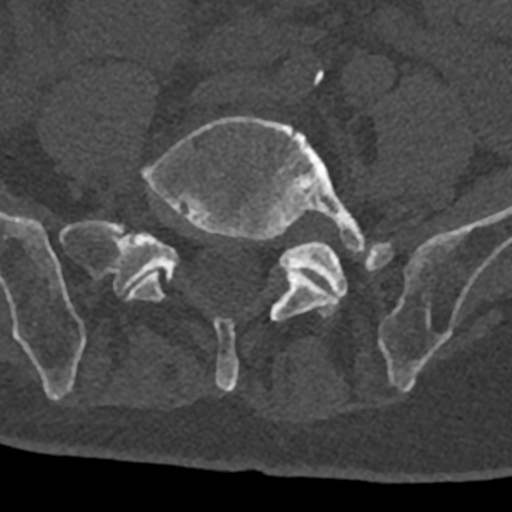
CT including the spine, one axial slice. Slice 183 of 797 in the series (ordered by position). Bone window (W 1800 / L 400 HU). 512 × 512 image matrix. Male patient, age 74 years. Case-level facts recorded for this patient, not image findings: primary cancer: renal.
Outlined on this slice (semi-automatic segmentation, software-assisted and operator-edited):
- L4 vertebra: bounding box <314,70,324,85> (left, top, right, bottom; pixels)
- L5 vertebra: <127,116,365,392>